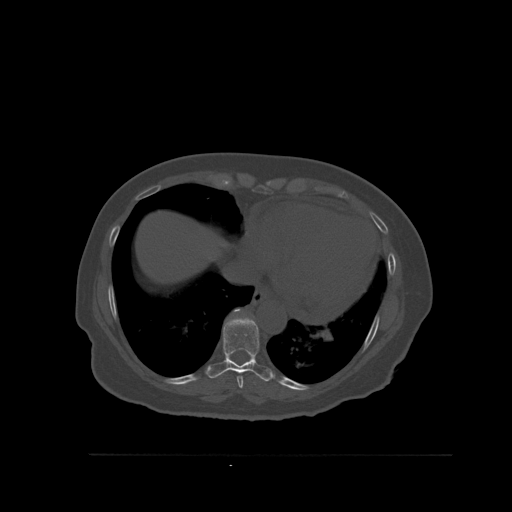
CT including the spine, one axial slice. Position 336 of 527 along the scan axis. Bone window (W 1800 / L 400 HU). 512 × 512 image matrix, field of view 470 × 470 mm. Female patient, age 73 years. Case-level facts recorded for this patient, not image findings: primary cancer: breast.
Annotated regions visible in this slice (semi-automatic segmentation, software-assisted and operator-edited):
- T8 vertebra: bounding box [x1, y1, x2, y2] px = [237, 376, 243, 389]
- T9 vertebra: [206, 316, 273, 382]